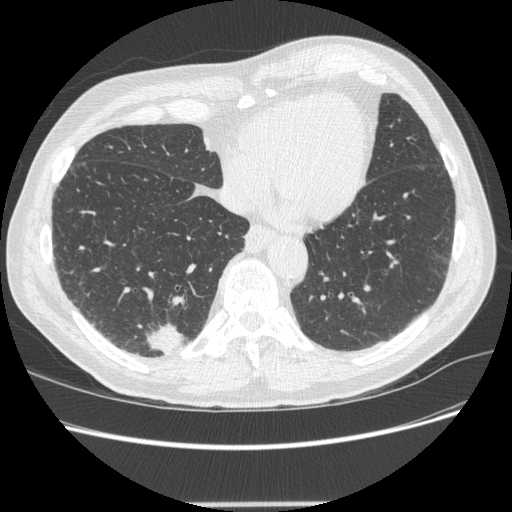
Low-dose screening chest CT, one axial slice; position 71 of 245 along the scan axis; reconstruction kernel STANDARD; 120 kVp; lung window (W 1500 / L -600 HU); 1.25 mm slice thickness; 512 × 512 image matrix, field of view 372 × 372 mm.
Annotated regions visible in this slice (expert manual segmentation):
- lesion 1 (tumor, lower lobe of right lung): bounding box (x1, y1, x2, y2) in pixels: (147, 324, 184, 355)